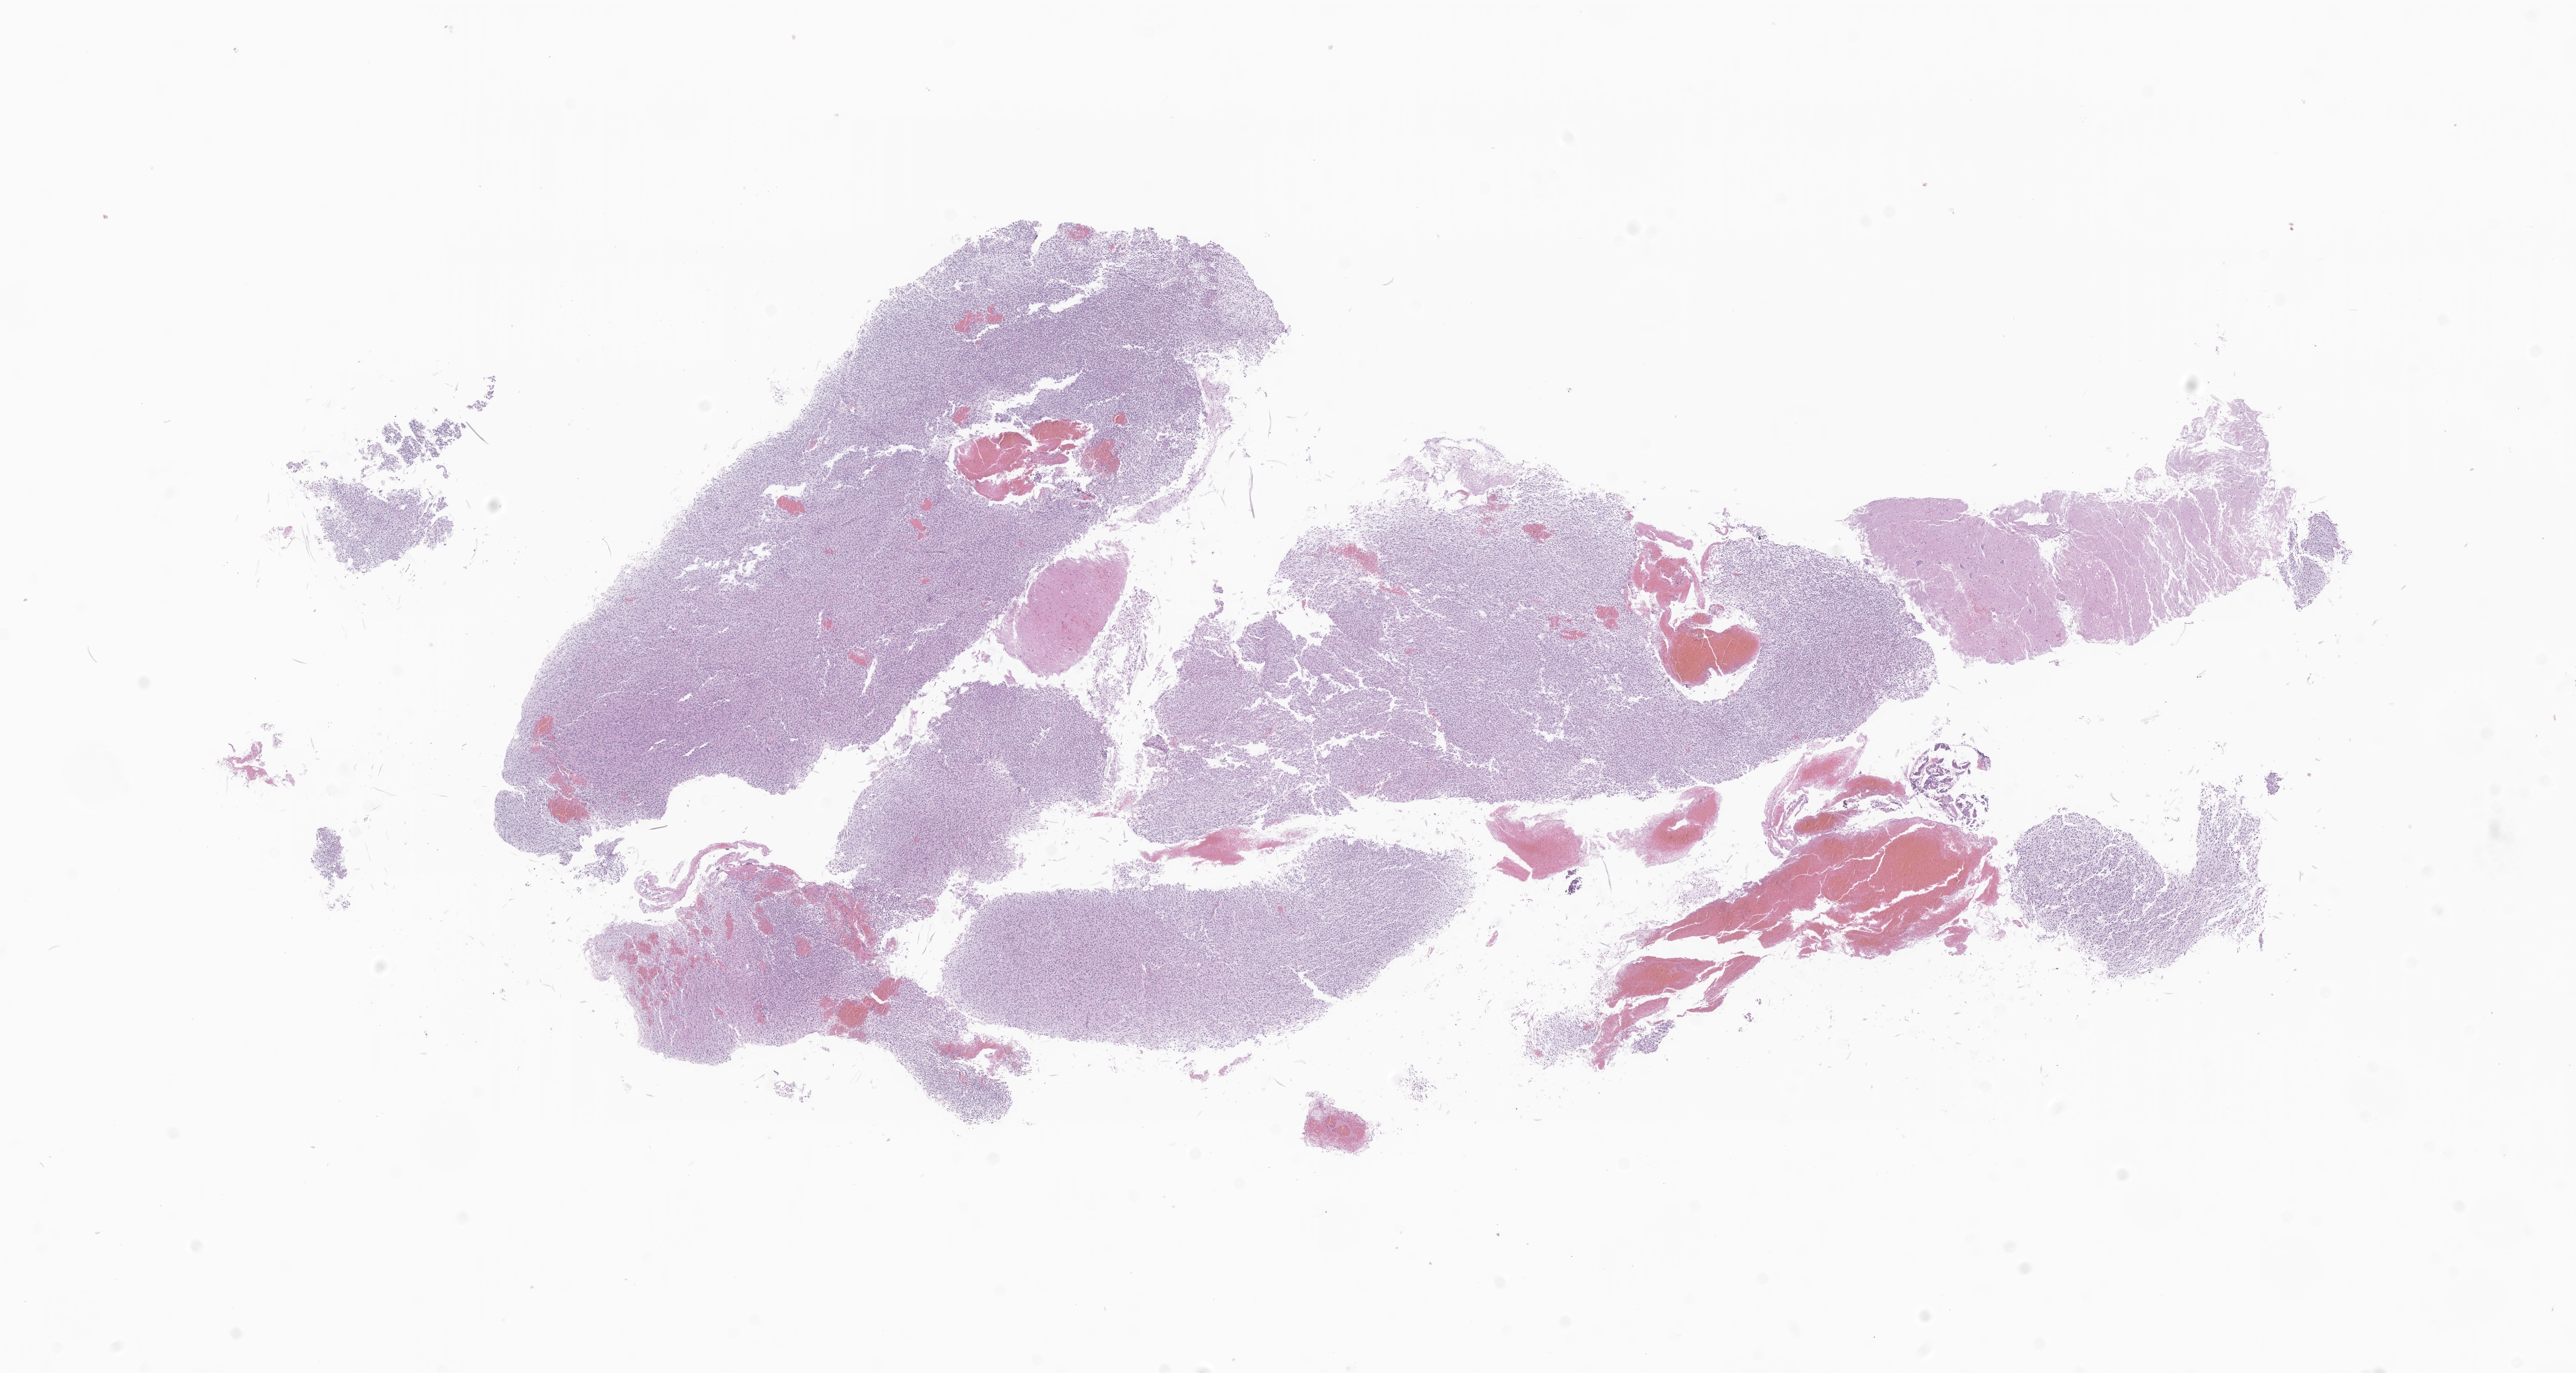
Haematoxylin and eosin whole-slide image of tumor tissue from the brain stem, shown as a low-resolution overview of the whole scanned area (about 21.8 x 11.6 mm); formalin-fixed, paraffin-embedded (FFPE) tissue. Male patient, age 106 months (8 years 10 months).
- diagnosis (ICD-O-3 morphology term): Glioma, malignant